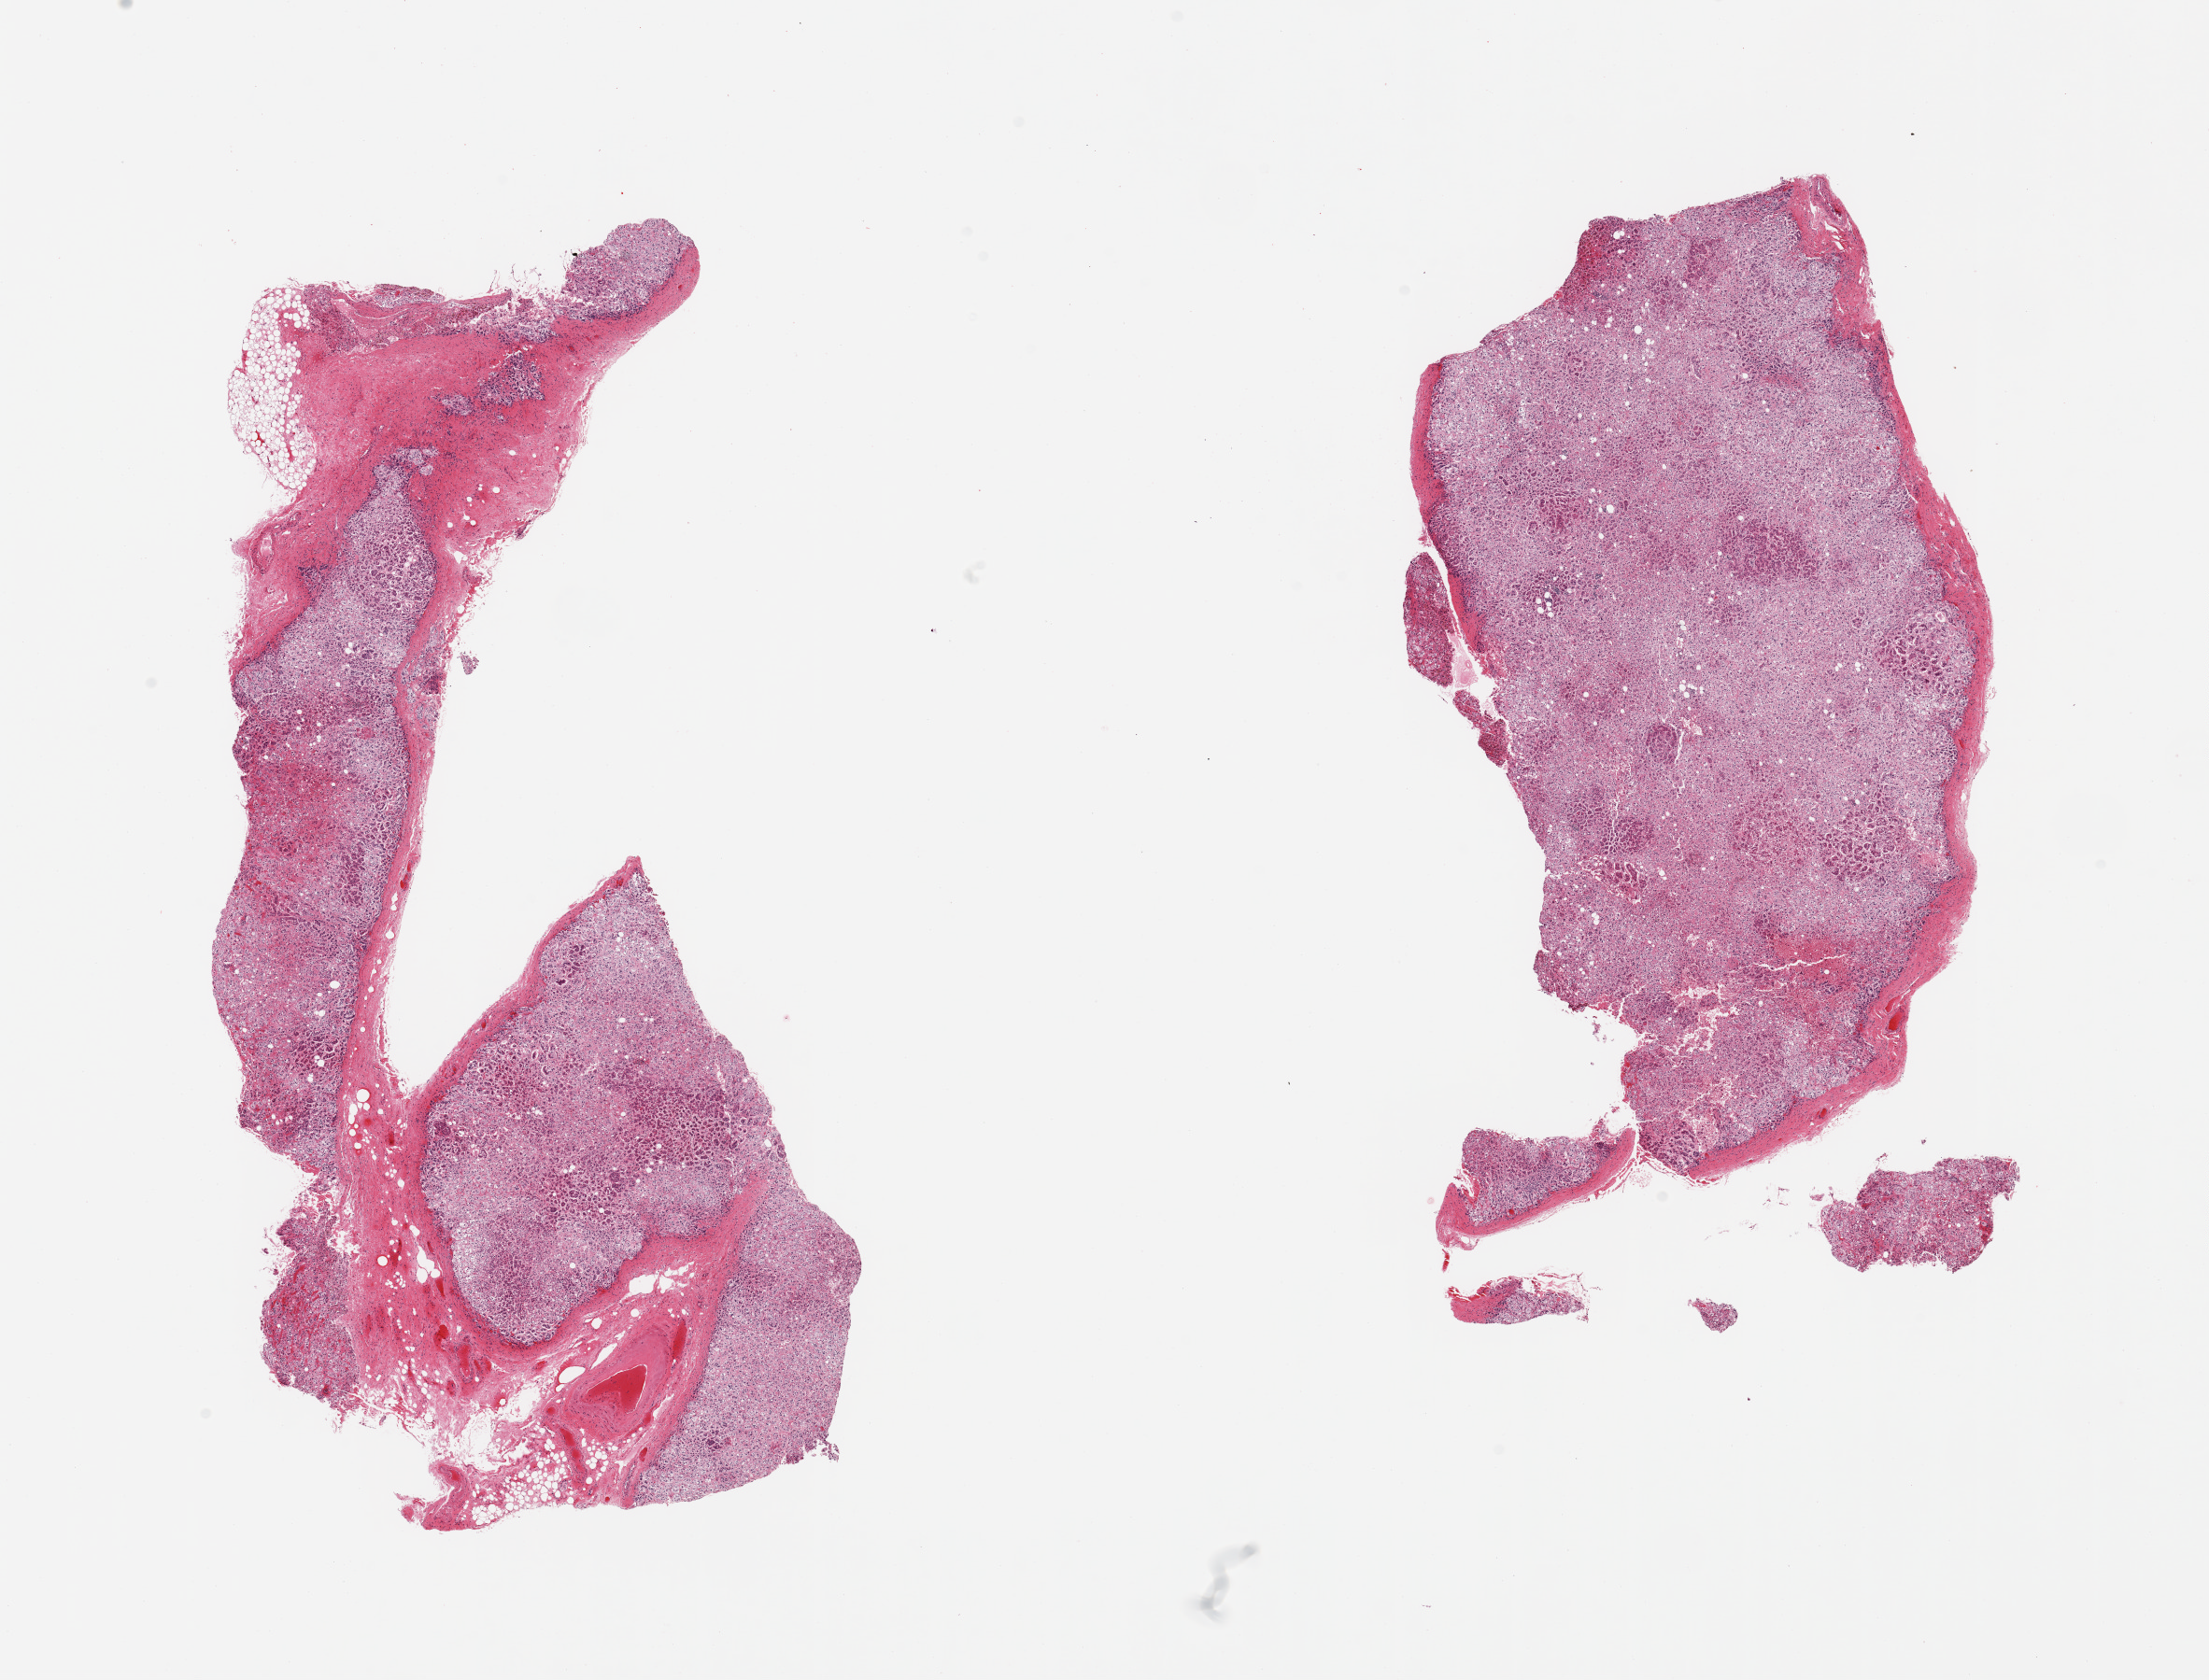
Digitized hematoxylin and eosin (H&E)-stained section, brightfield — shown as a low-resolution overview of the whole scanned area (about 18.7 x 14.2 mm, acquisition: 20x scan); PAXgene-fixed, paraffin-embedded tissue; sampled site (target tissue): adrenal gland; donor tissue sample.
* review note (as recorded): 2 pieces; cortex; up to 10% congested fibrovascular component on one piece